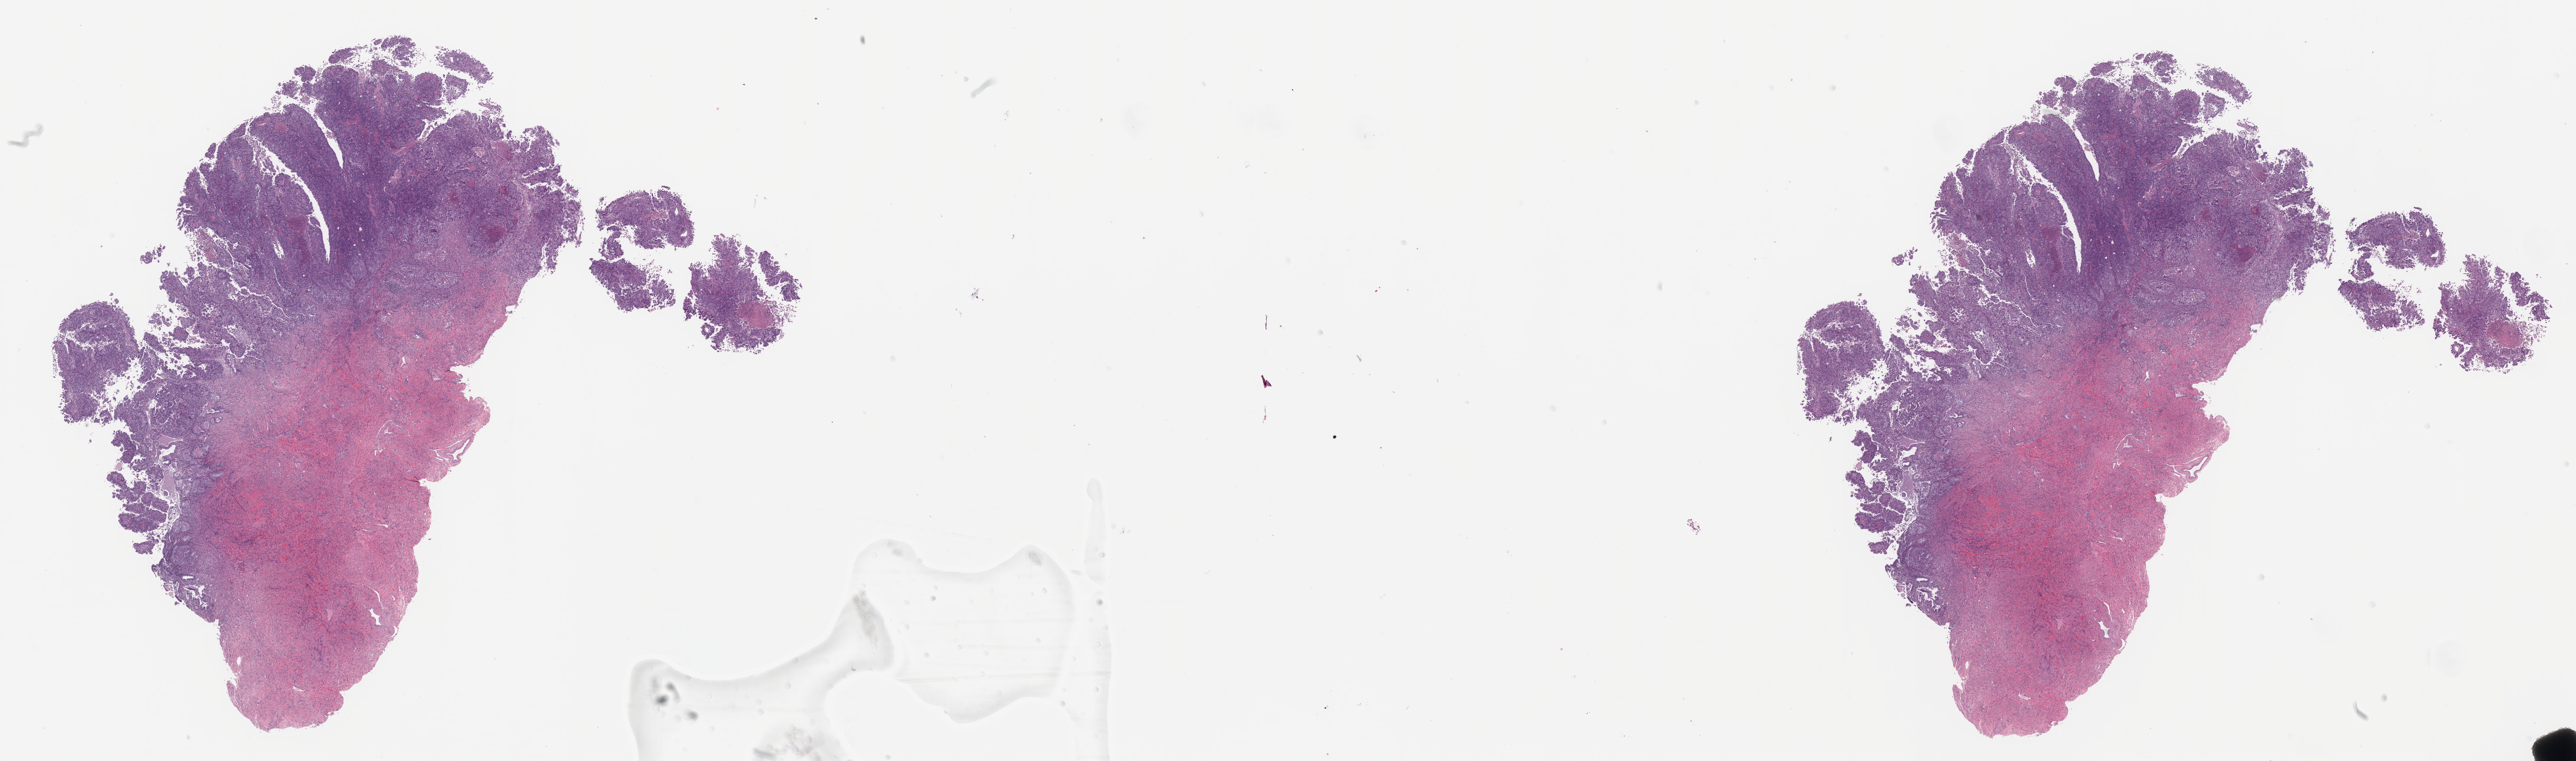
Digitized H&E-stained tissue section (whole slide), a low-resolution overview of the entire scanned area, about 35.0 x 10.3 mm (slide scanned at 20x). Formalin-fixed paraffin-embedded (FFPE) diagnostic section. Uterus, primary tumour sample. Female patient. Histologic grade: G3 (poorly differentiated).
Pathologic diagnosis: Endometrioid adenocarcinoma, NOS (endometrium). FIGO stage: IIIC.